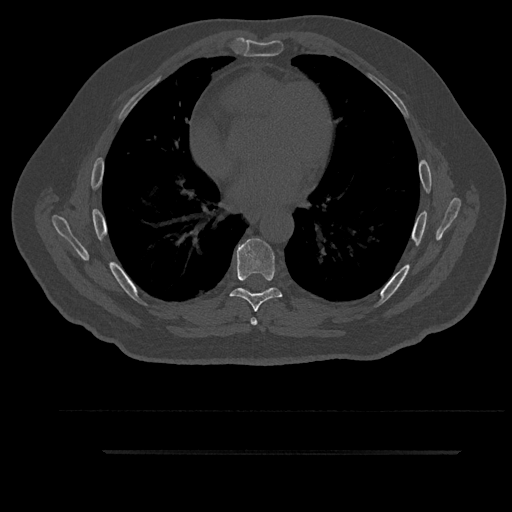
CT including the spine, one axial slice; position 527 of 797 along the scan axis; reconstruction kernel Br40s/3; 120 kVp; bone window (W 1800 / L 400 HU); 0.5 mm slice thickness; 512 × 512 image matrix, field of view 432 × 432 mm. Male patient, age 63 years. From the clinical record (not read from this slice): primary cancer: renal; vertebrae with lytic lesions (as recorded): T8.
Annotated regions visible in this slice (semi-automatically segmented with operator editing):
- T6 vertebra: bounding box [x1, y1, x2, y2] px = [251, 289, 269, 325]
- T7 vertebra: [230, 238, 282, 312]